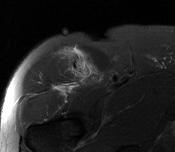
MRI of an extremity soft-tissue mass, one axial slice; slice 114 of 116 in the series (ordered by position); T2-weighted fat-saturated; MR volume resampled by the dataset authors to the PET/CT grid (not the native acquisition matrix); 3.27 mm slice thickness; 175 × 152 image matrix, field of view 171 × 148 mm. Male patient. Case-level facts recorded for this patient, not image findings: histological type: pleiomorphic leiomyosarcoma; grade: intermediate; site of the primary tumour: right thigh.
Annotated regions visible in this slice (expert contour drawn on MRI and transferred to this co-registered scan by the dataset authors):
- gross tumour volume including surrounding oedema: box from (x=70, y=56) to (x=91, y=78) px